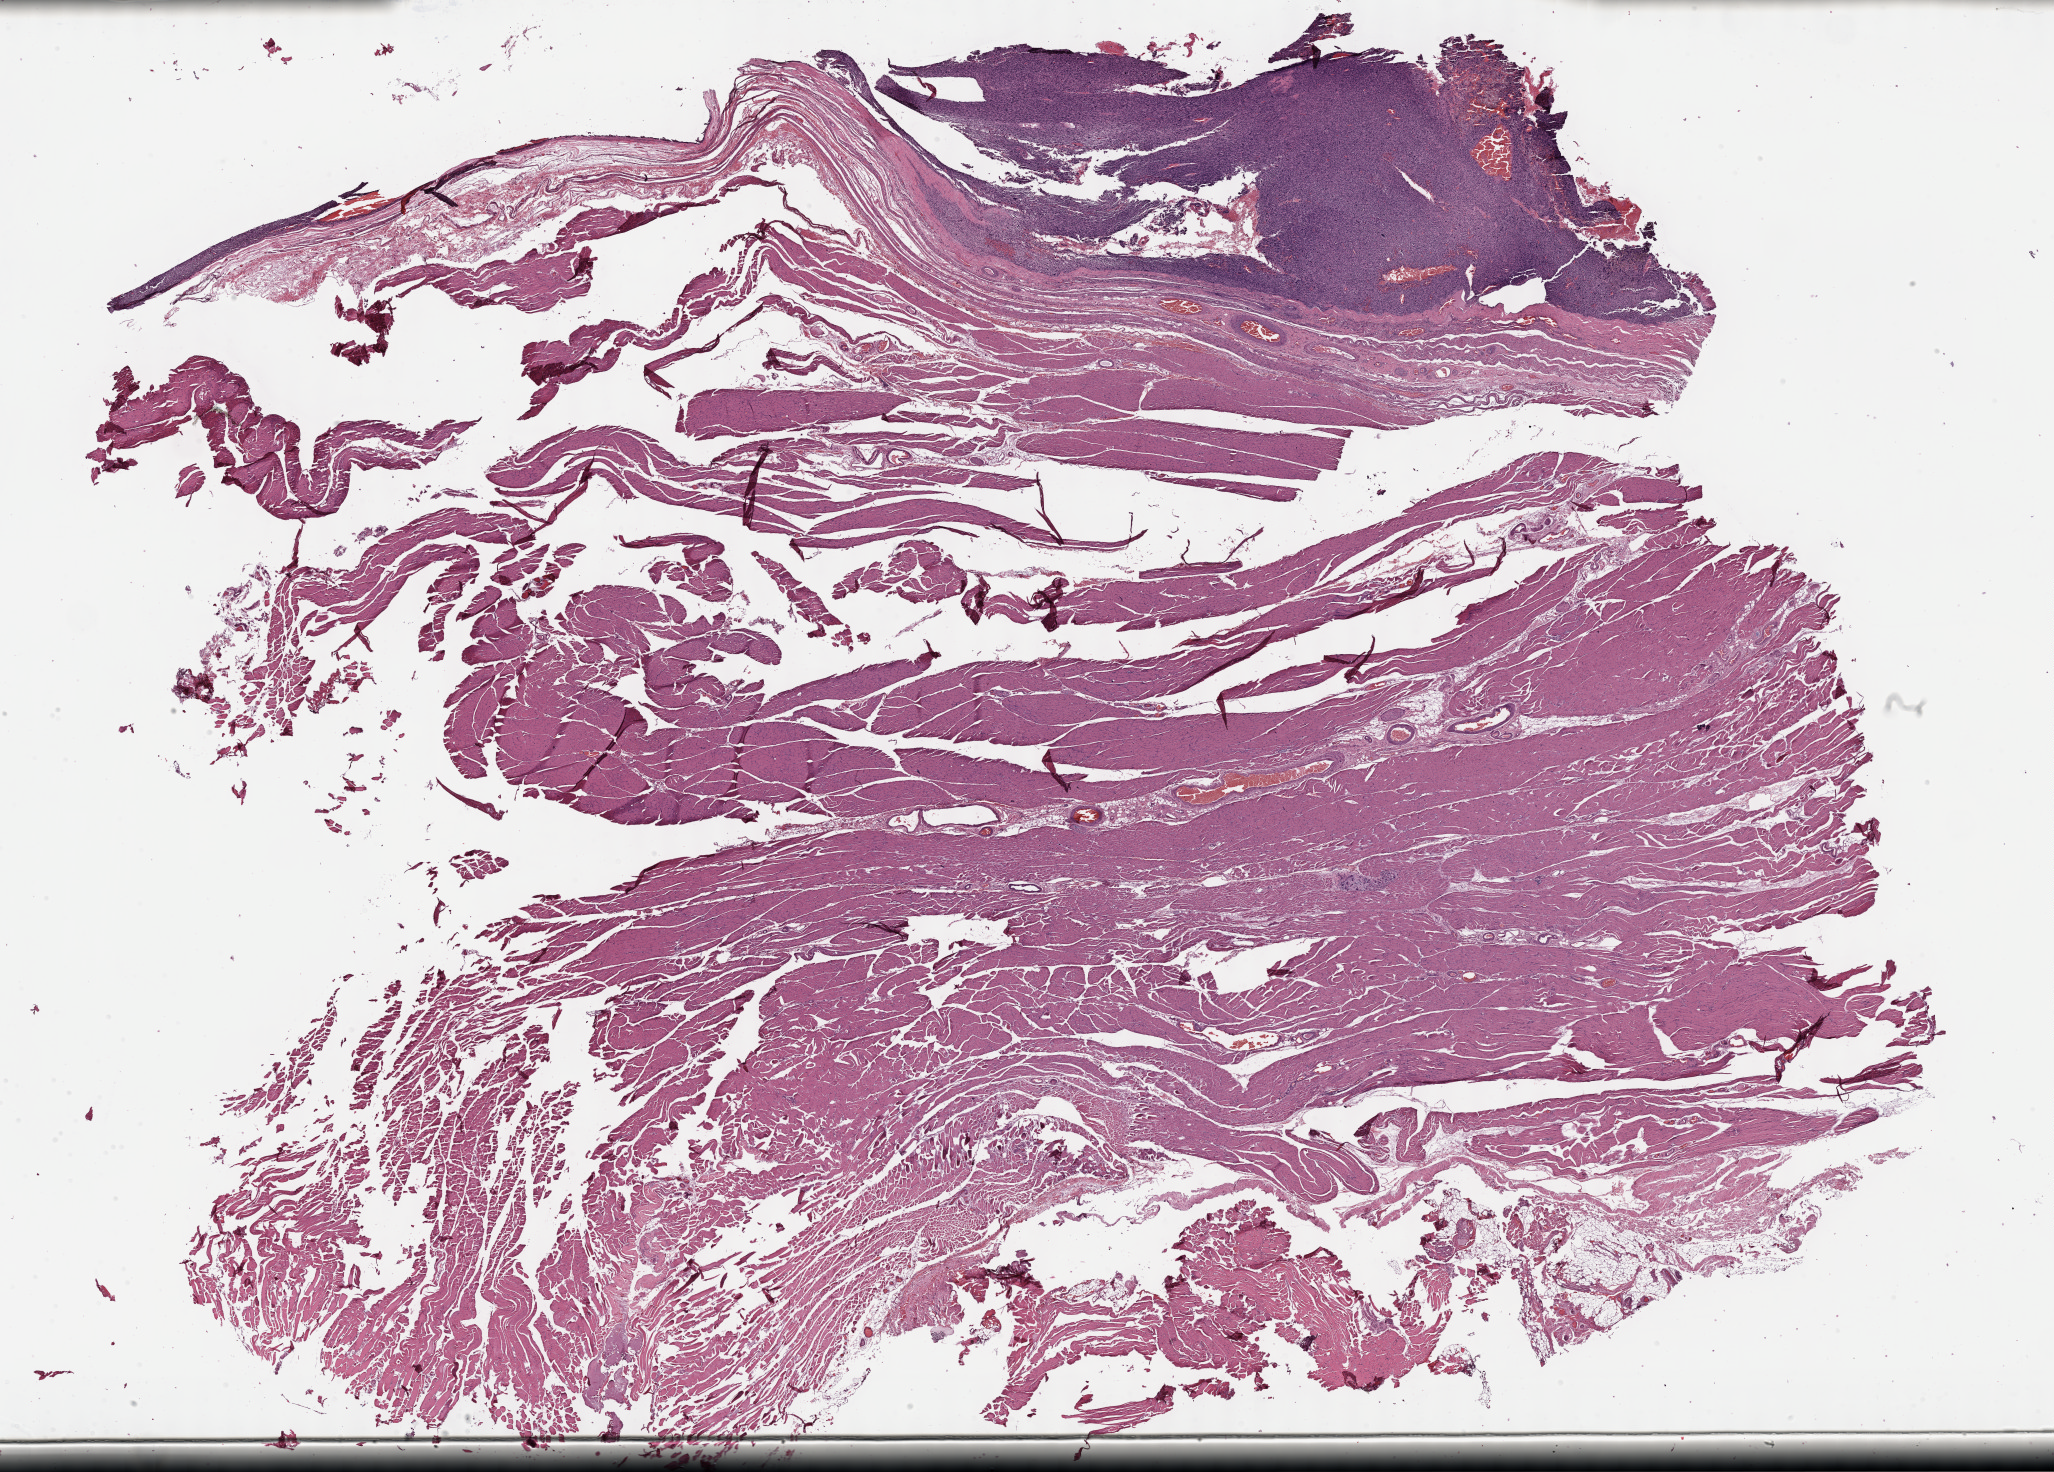
Whole-slide histology image, H&E — a low-resolution overview of the entire scanned area, about 33.2 x 23.8 mm, FFPE section, sample: primary tumour, connective, subcutaneous and other soft tissues. Female, age 80 years at initial diagnosis.
Histologic diagnosis: Undifferentiated sarcoma.